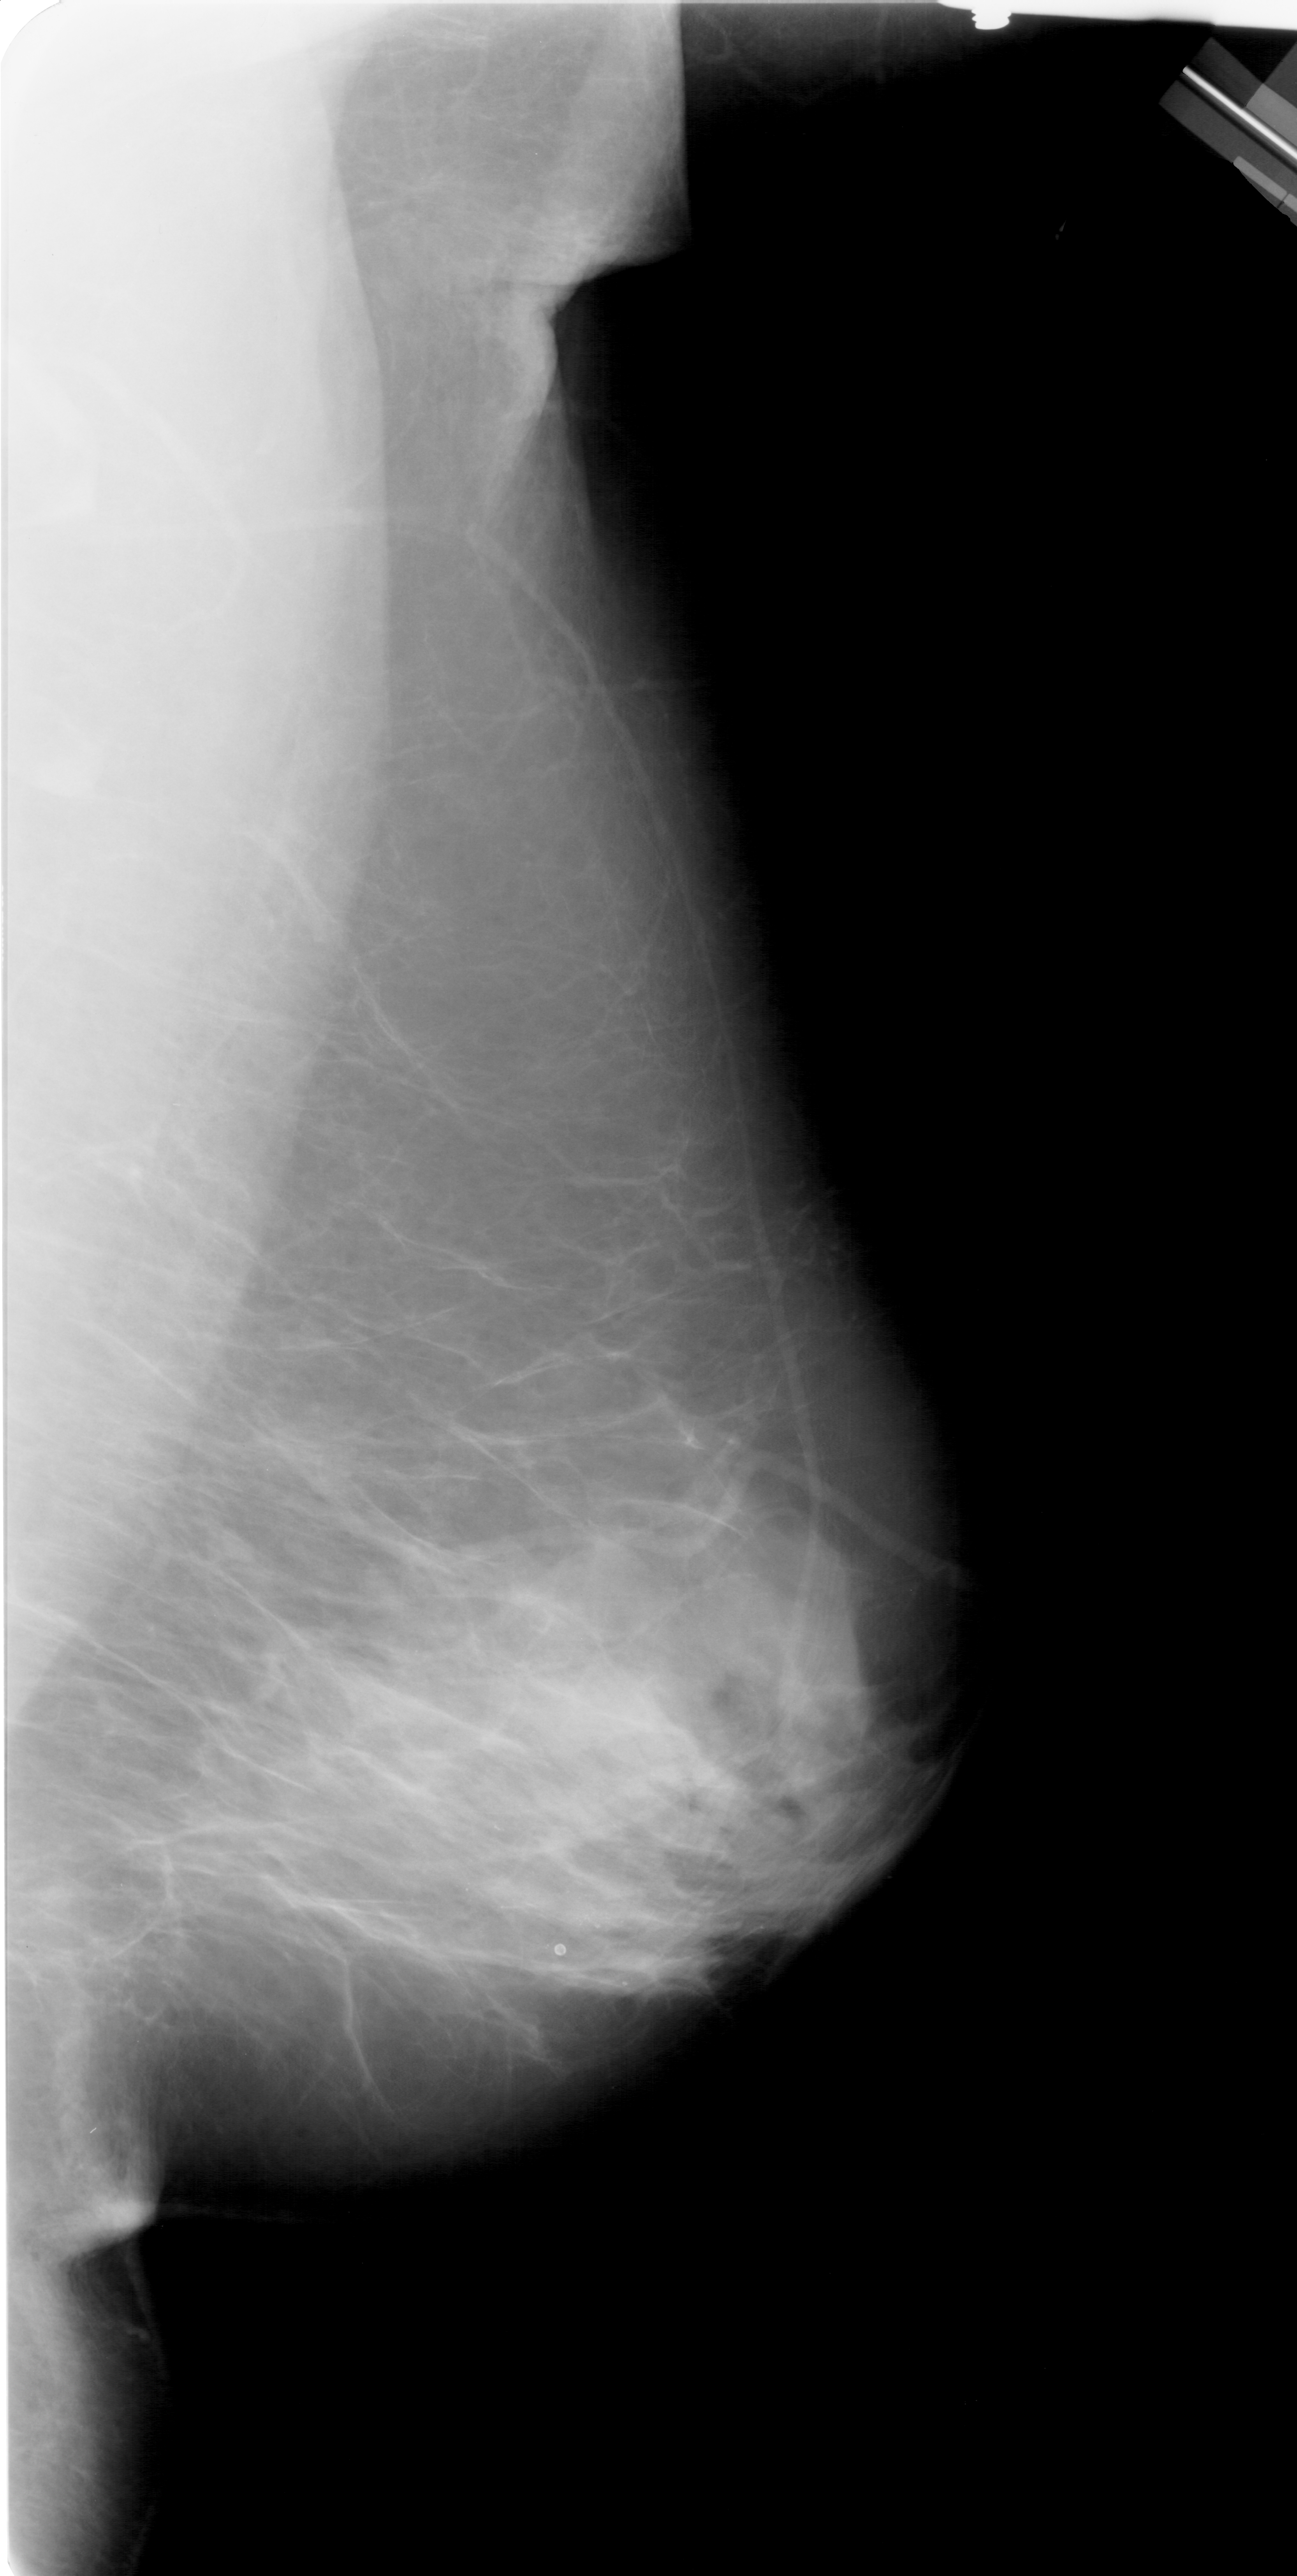
Mammogram (digitized film), right breast, mediolateral oblique (MLO) view, BI-RADS breast density category 4 (scale 1–4).
Marked findings (only marked abnormalities are described; nothing is implied about the rest of the image): calcifications, morphology pleomorphic, distribution linear; BI-RADS assessment category 4; subtlety rating 3 on a 1 (subtle) to 5 (obvious) scale; pathology (as recorded): benign.